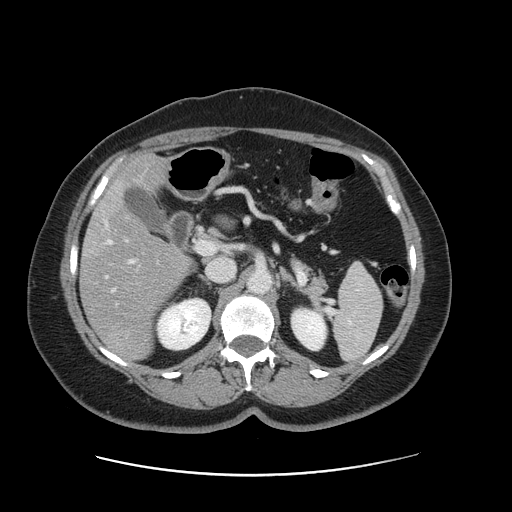
Contrast-enhanced abdominal CT, one axial slice; slice 78 of 161 in the series (ordered by position); 120 kVp; soft-tissue window (W 400 / L 40 HU); 512 × 512 image matrix. Female patient, age 62 years. From the clinical record (not read from this slice): diagnosis: colorectal cancer liver metastases, imaged before liver resection; multiple liver metastases: no; largest metastasis: 2.5 cm.
Outlined on this slice (outlined manually by an expert reader):
- hepatic veins: box from (x=106, y=222) to (x=115, y=292) px
- liver: (x=82, y=156)–(x=190, y=361)
- planned liver remnant (the part of the liver to remain after resection): (x=115, y=156)–(x=164, y=192)
- portal vein (with intrahepatic branches): (x=126, y=240)–(x=134, y=263)